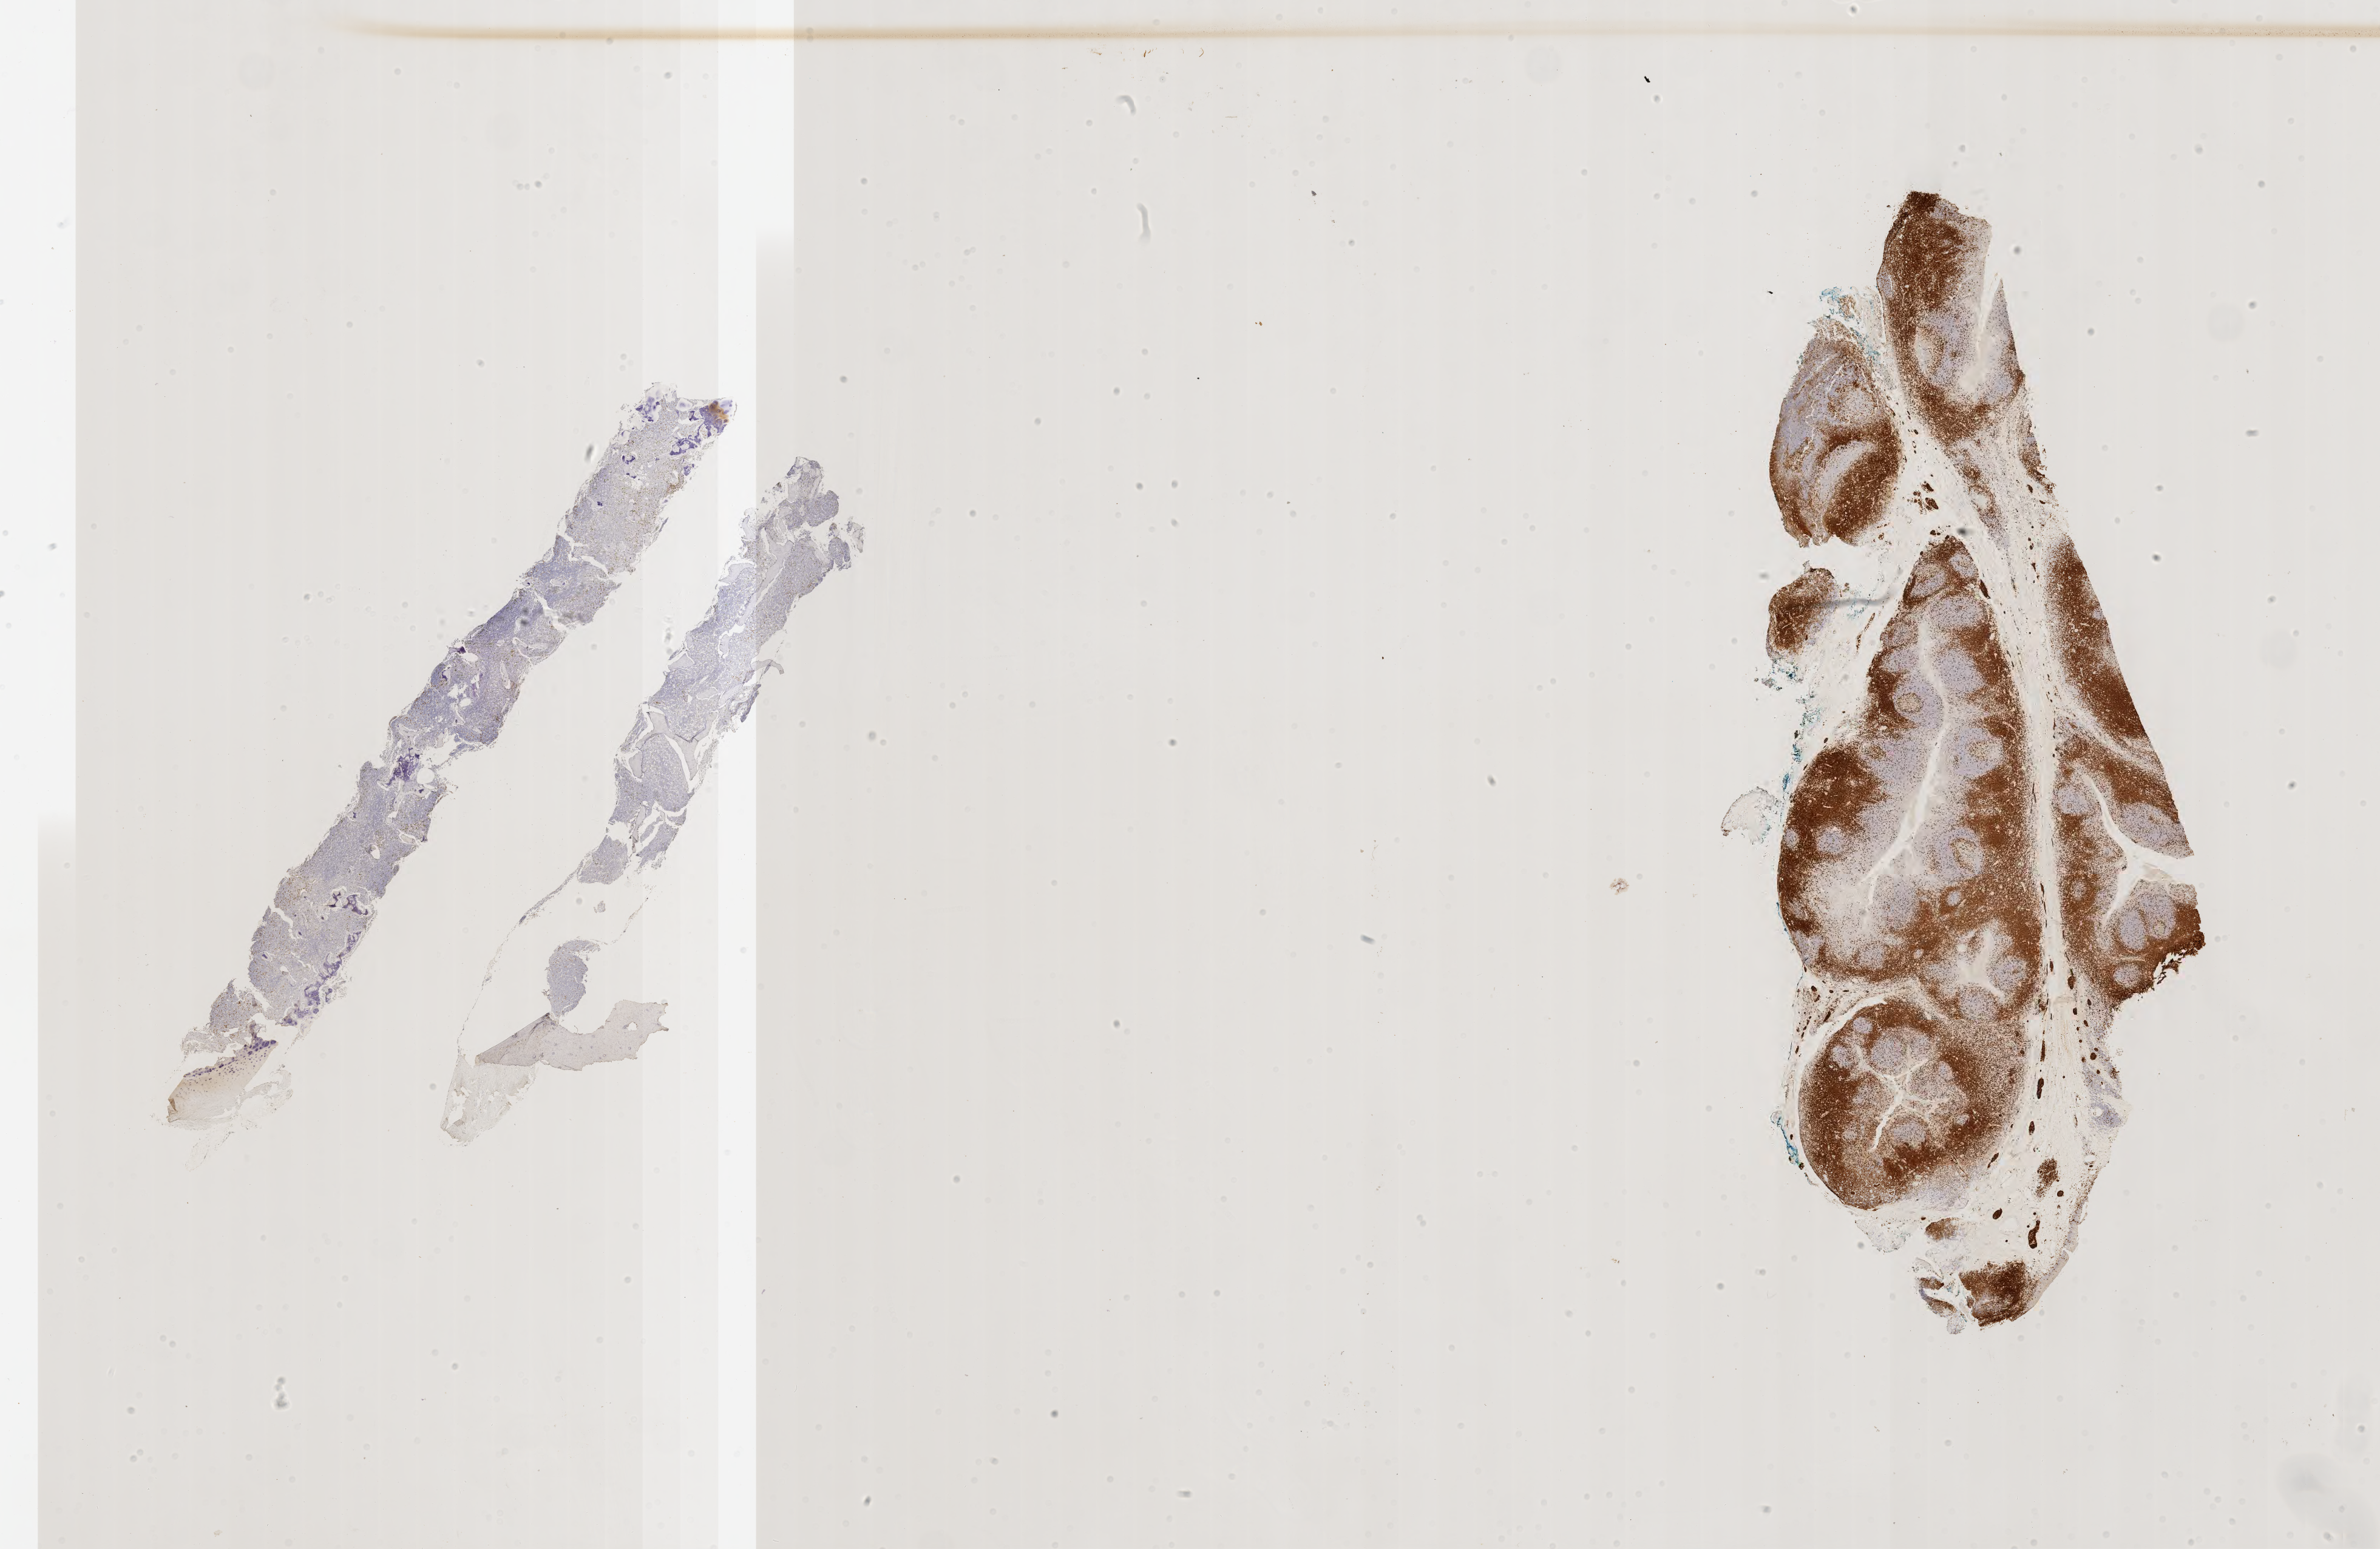
Whole-slide image, immunohistochemical stain for CD3, a low-resolution overview of the entire scanned area, about 31.7 x 20.6 mm, tumor tissue, anatomic site: bone marrow. Patient: male, age 16 years.
Diagnosis: Burkitt lymphoma, NOS.